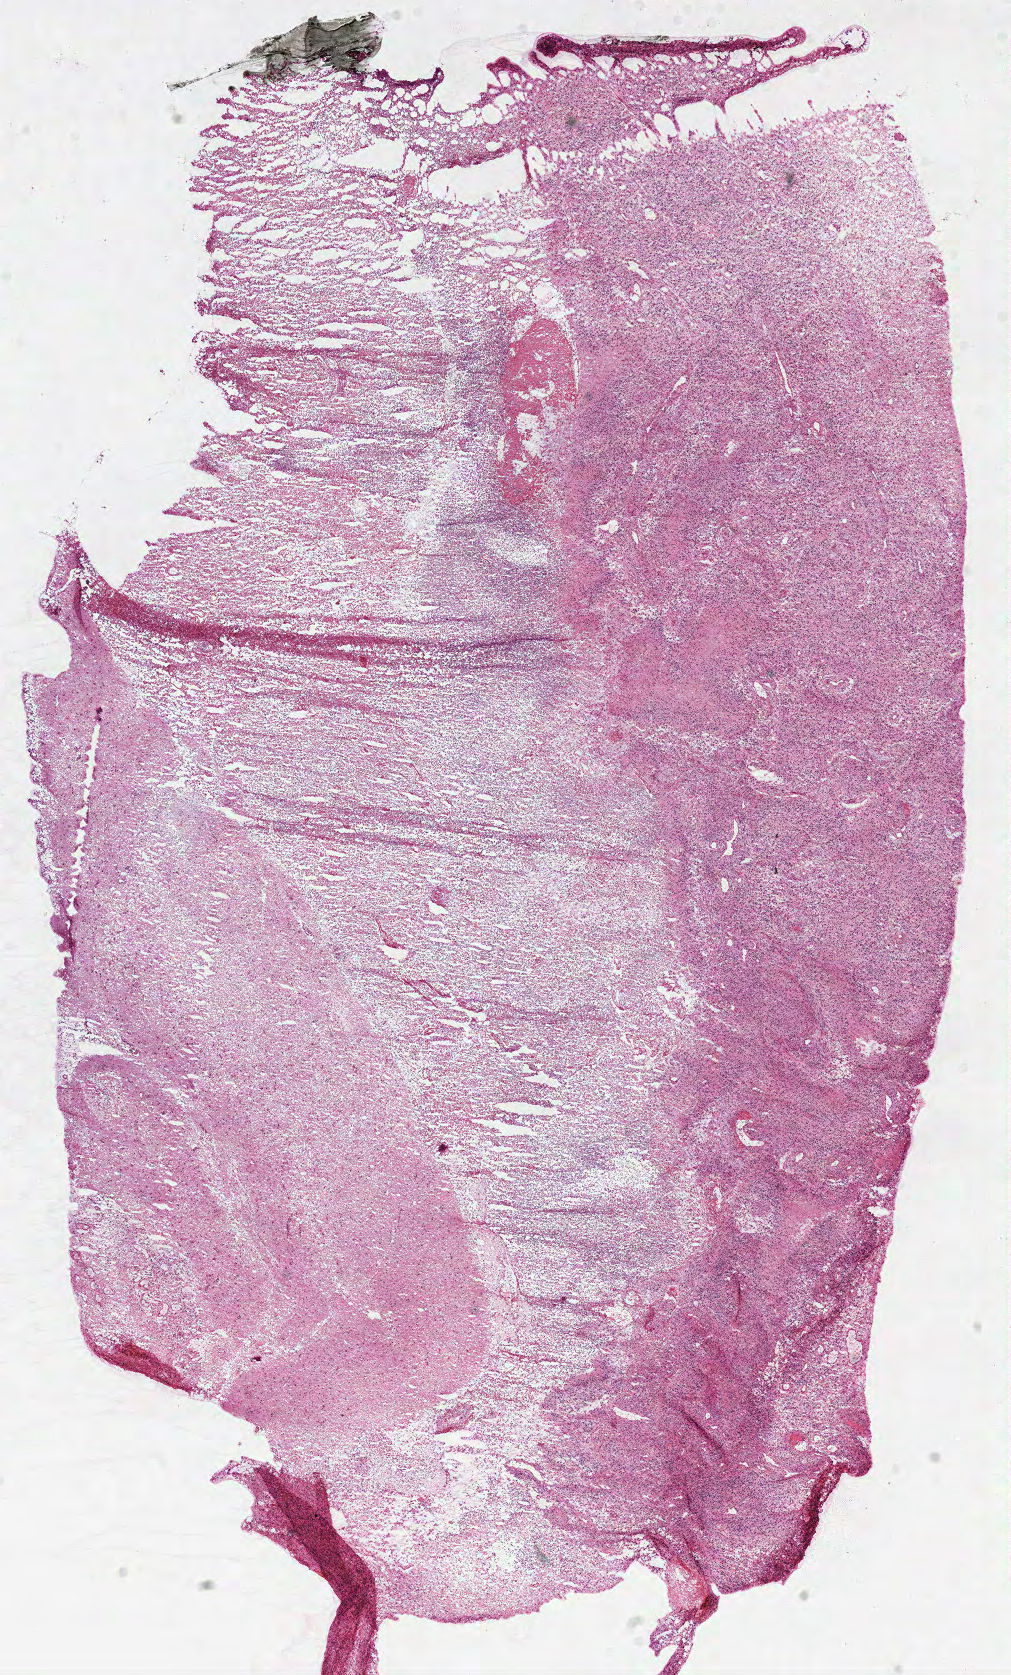
Digitized H&E tissue section (whole slide) — whole scanned area (about 8.0 x 13.2 mm) shown as a low-resolution overview; frozen section from the top of the tissue portion; brain, primary tumour sample. Patient: male, age at initial diagnosis 51 years. Composition of this section per pathologist review: tumour cells 55%, tumour nuclei 75%, normal cells 0%, stromal cells 0%, necrosis 45%.
Histologic diagnosis: Glioblastoma.